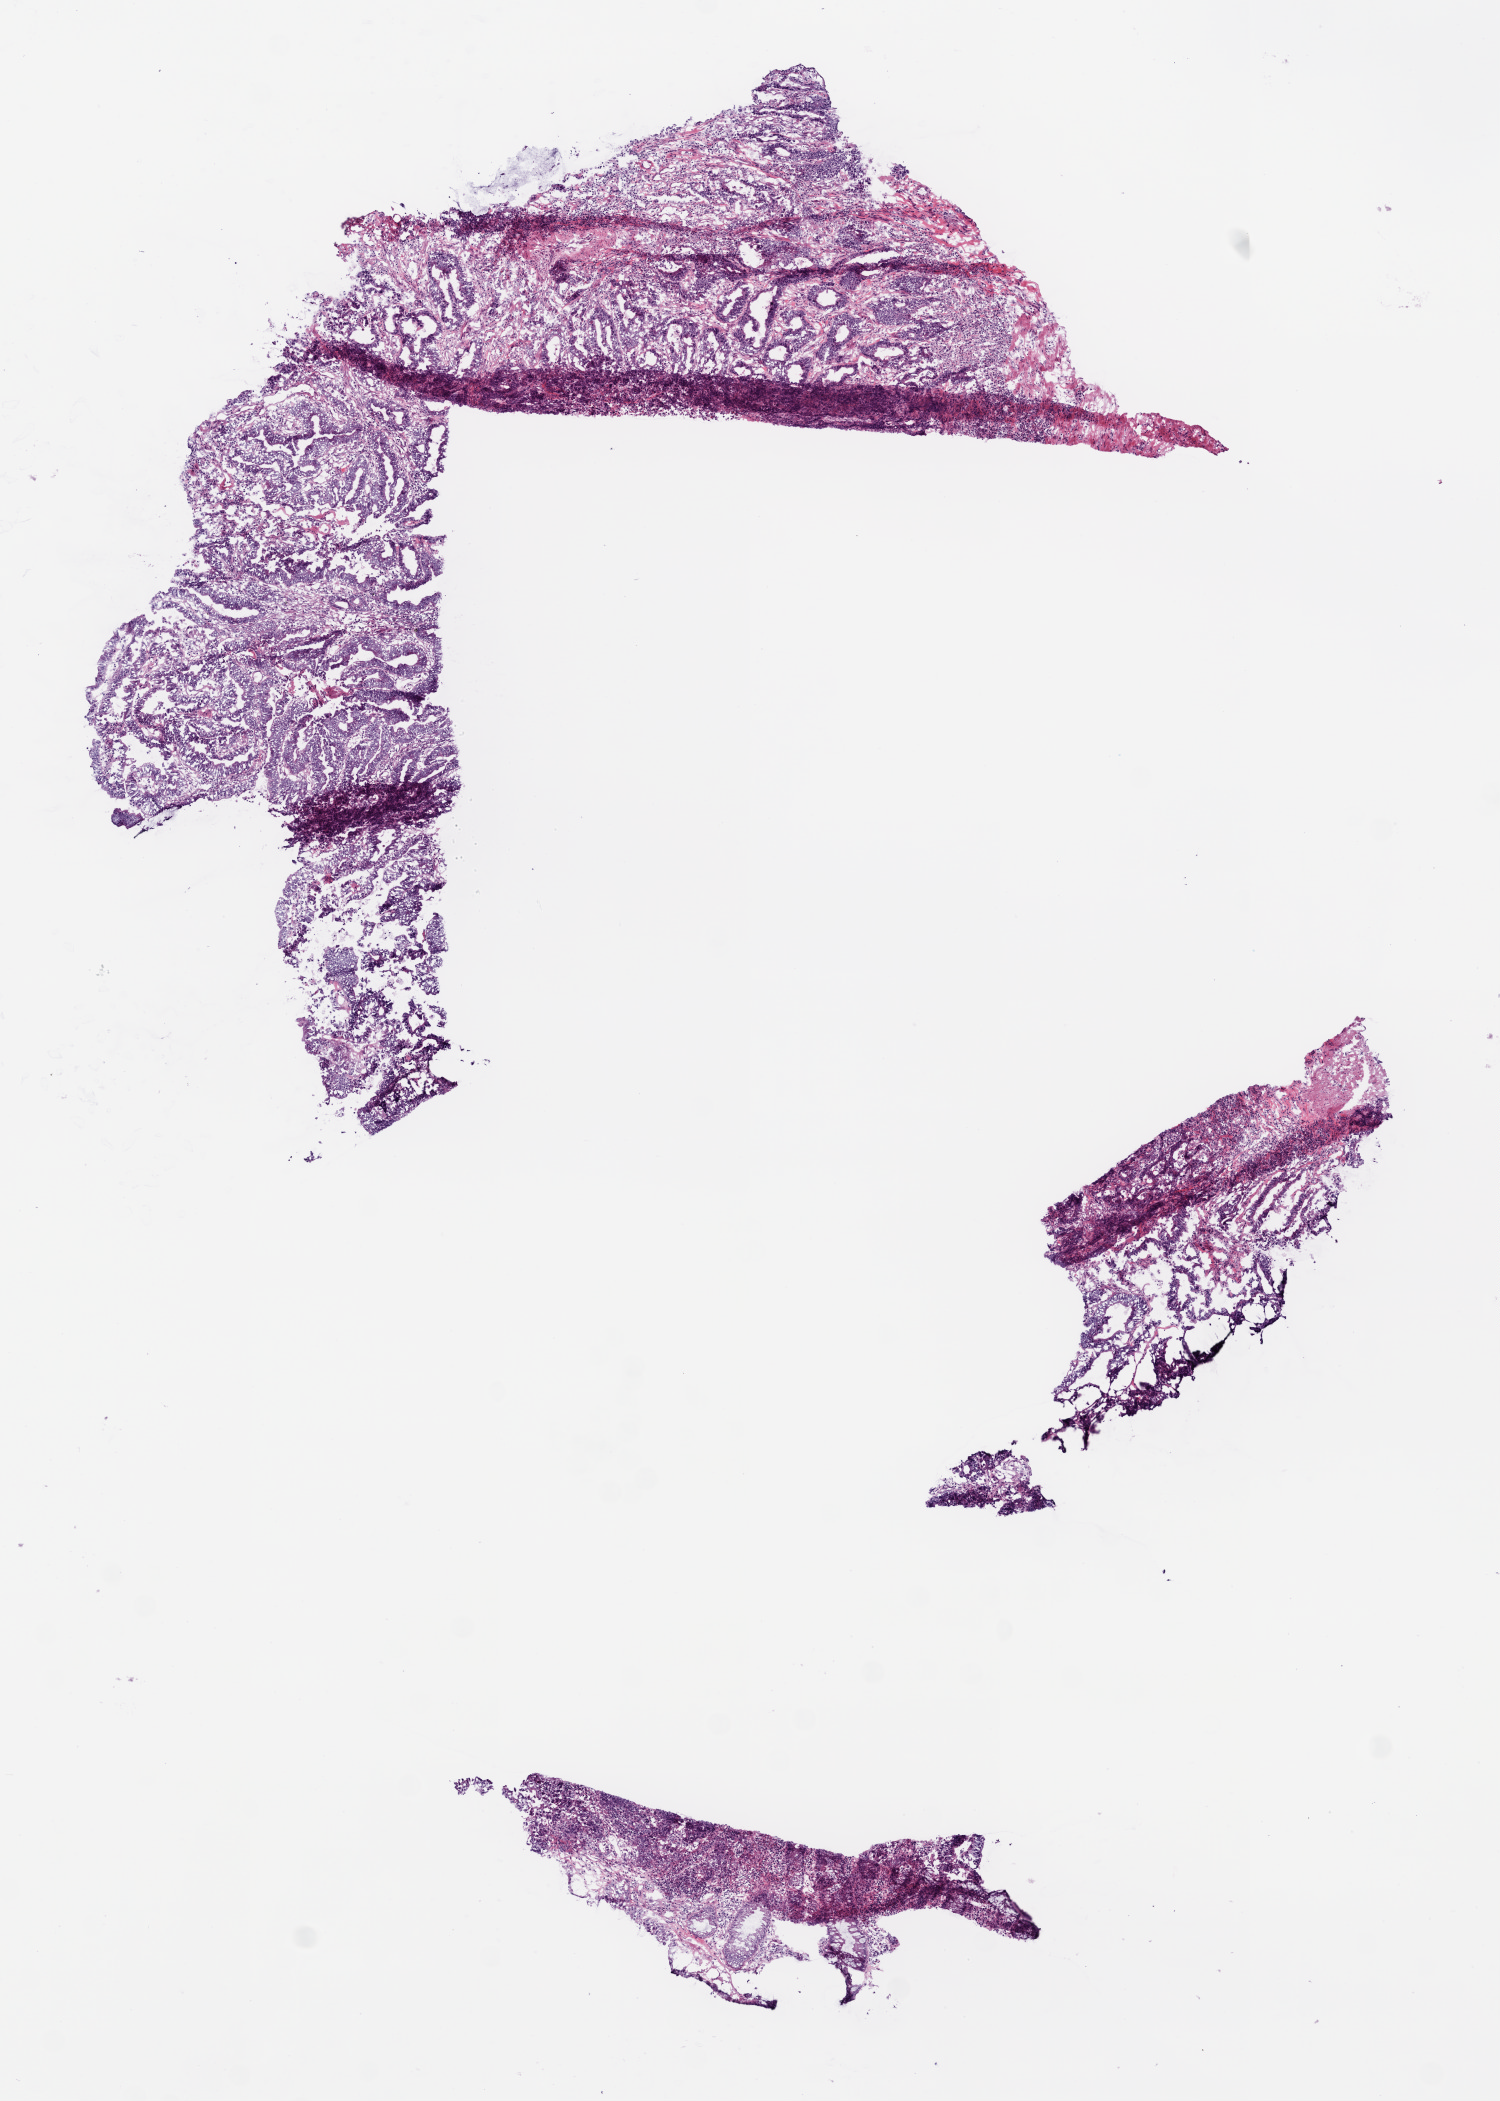
Hematoxylin and eosin (H&E) stained whole-slide image, low-resolution overview of the scanned area, about 6.0 x 8.4 mm, frozen section, primary tumour sample from the colon. Patient: female, age at initial diagnosis 61 years. Pathologist review of this section (percent, as recorded): tumour cells 90%, tumour nuclei 85%, normal cells 4%, stromal cells 0%, necrosis 0%. Inflammatory infiltration, as recorded: lymphocyte infiltration 6%, neutrophil infiltration 5%.
Histologic diagnosis: Adenocarcinoma, NOS (sigmoid colon). TNM: T3 N0 M0. AJCC pathologic stage: IIA (6th edition). Lymph nodes positive (case pathology): 0 of 12 examined.